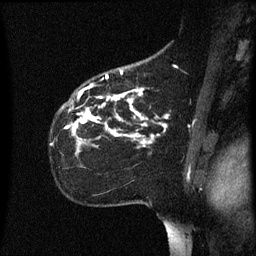
Breast MRI (dynamic contrast-enhanced), one sagittal slice. Slice 43 of 60 in the series (ordered by position). Dynamic contrast-enhanced series, image 2 of 3 at this slice position (ordered by acquisition). 1.5 T. TE 4.2 ms, TR 8.4 ms. 2.2 mm slice thickness. 256 × 256 image matrix, field of view 200 × 200 mm. Patient: female, 35 years. From the clinical record (not read from this slice): setting: breast cancer imaged before/during neoadjuvant chemotherapy; receptor status: HER2-positive.
Structures marked on this image (semi-automatic segmentation, software-assisted and operator-edited):
- analysis volume of interest (the breast-tissue region the enhancement analysis was run in; not a lesion): bounding box (x1, y1, x2, y2) in pixels: (51, 78, 170, 155)
- tumour enhancement mask (voxels above the 70 % enhancement threshold inside the analysis volume of interest): (66, 90, 169, 145)